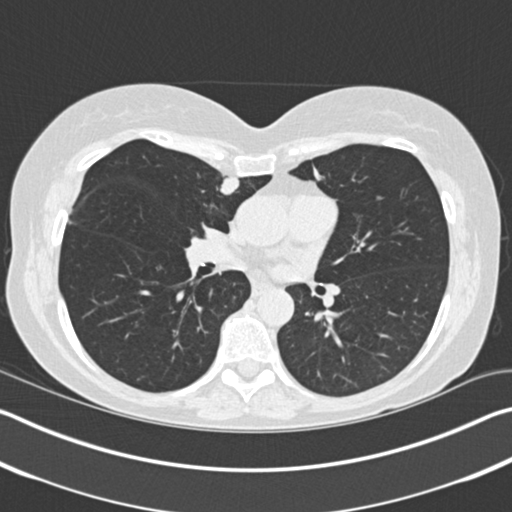
Chest CT (low-dose screening protocol), one axial image. Baseline annual screen. Lung window (W 1500 / L -600 HU). Standard (soft-tissue) reconstruction kernel (B30f). 120 kVp. Slice 87 of 183 in the series. 512 × 512 image matrix, field of view 340 × 340 mm. Female, age 61 years at enrolment. Former smoker at enrolment.
Expert reader's lesion annotation, box from (x=201, y=169) to (x=247, y=210) px. The screening reader recorded 2 non-calcified nodules or masses ≥4 mm on this exam (right upper lobe, right upper lobe); which of them this box marks is not recorded. Official screen result: positive, change unspecified: nodule(s) >= 4 mm or enlarging nodule(s), mass(es), or other non-specific abnormalities suspicious for lung cancer. Later outcome: lung cancer diagnosed 131 days after this screen — adenocarcinoma, NOS, right upper lobe, stage IA (AJCC 6th edition), 11 mm at pathology.